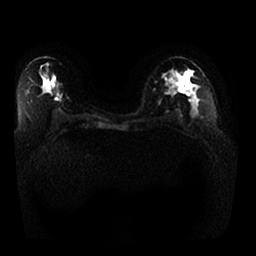
Breast MRI, one axial slice. Diffusion-weighted series; image 2 of 4 stored at this slice position (different b-values; order by instance number). 1.5 T. 4 mm slice thickness. 256 × 256 image matrix. Female patient.
Structures marked on this image (outlined manually by an expert reader):
- tumour on diffusion-weighted imaging: box from (x=179, y=82) to (x=185, y=90) px